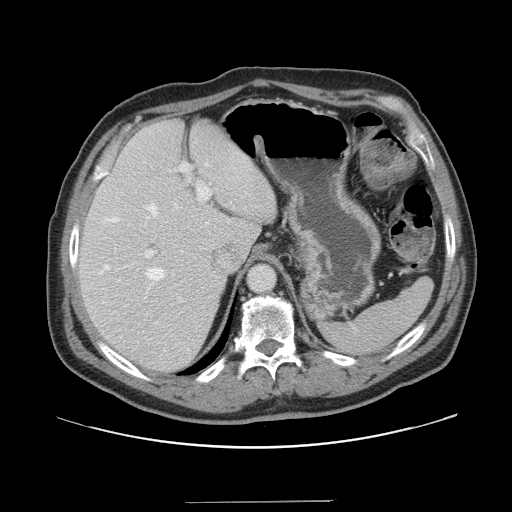
Contrast-enhanced abdominal CT, one axial slice. Slice 110 of 151 in the series (ordered by position). 120 kVp. Intravenous contrast given. Soft-tissue window (W 400 / L 40 HU). 2.5 mm slice thickness. 512 × 512 image matrix. Male patient, age 63 years. Case-level facts recorded for this patient, not image findings: diagnosis: colorectal cancer liver metastases, imaged before liver resection; multiple liver metastases: no; largest metastasis: 2.1 cm.
Structures marked on this image (expert manual segmentation):
- hepatic veins: bounding box (x1, y1, x2, y2) in pixels: (104, 163, 208, 281)
- liver: (79, 119, 276, 373)
- planned liver remnant (the part of the liver to remain after resection): (79, 118, 266, 373)
- portal vein (with intrahepatic branches): (145, 163, 212, 302)